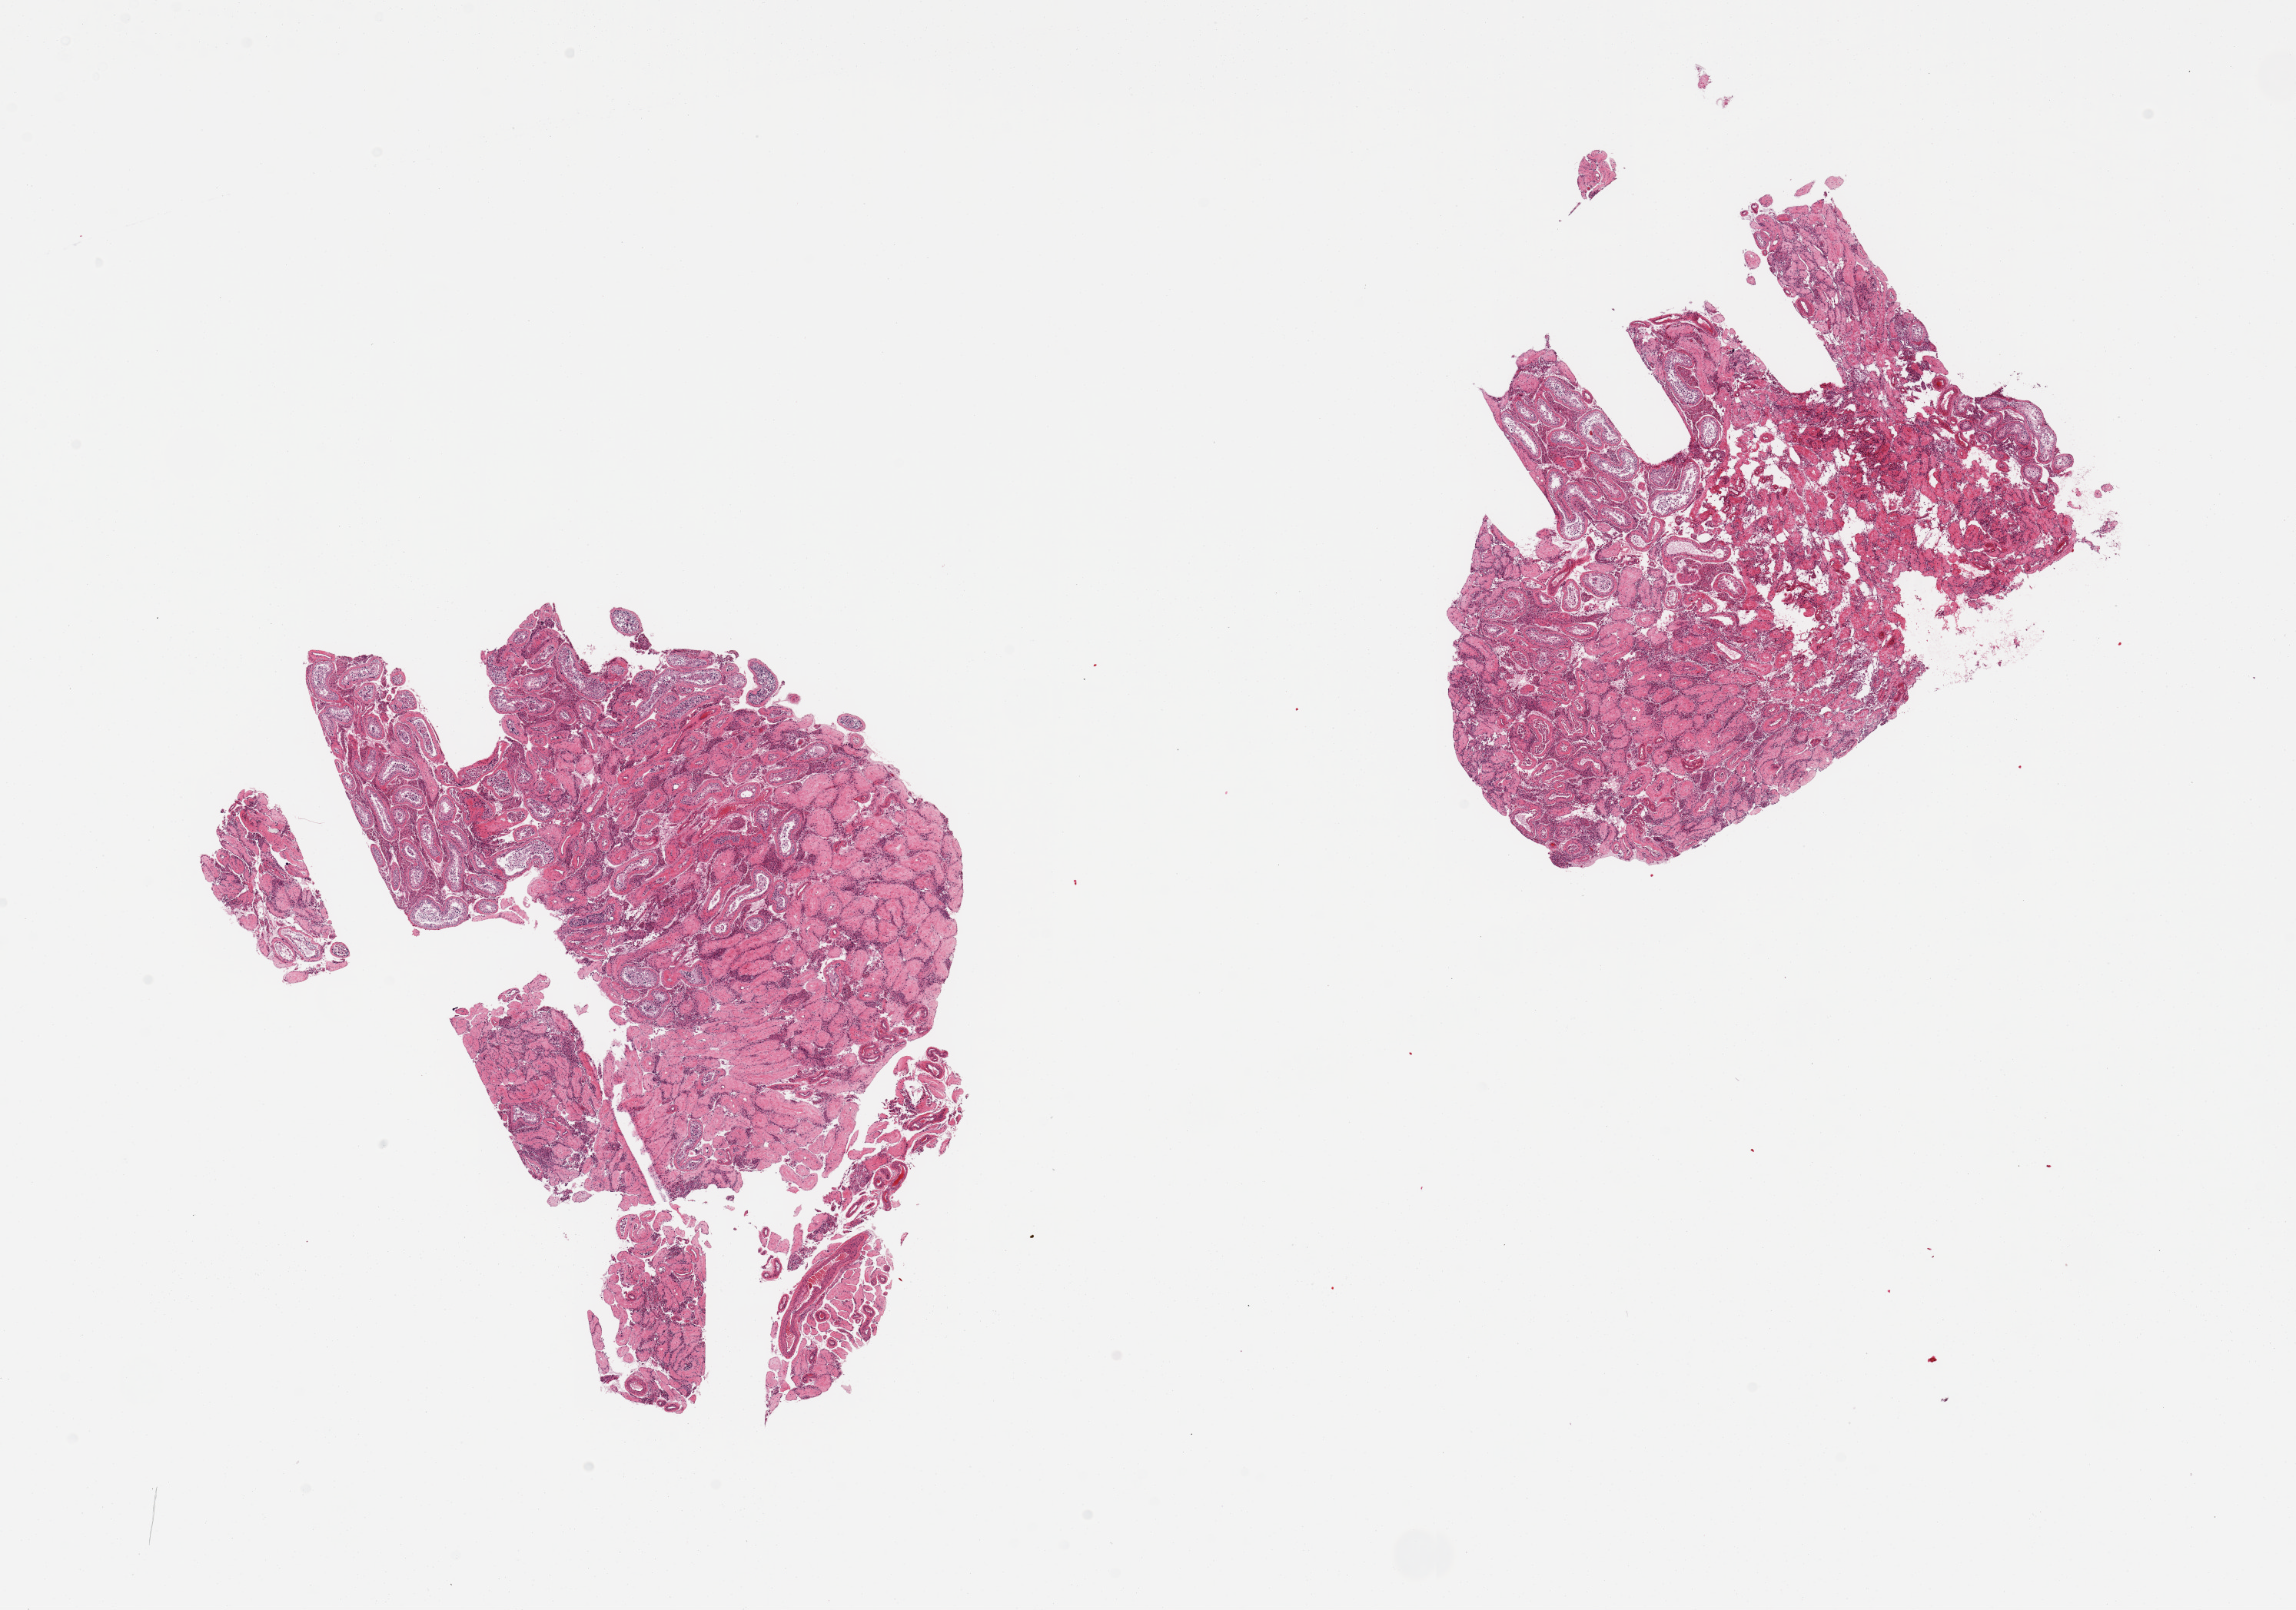
Hematoxylin and eosin (H&E) whole-slide image, brightfield, a low-resolution overview of the entire scanned area, about 23.6 x 16.6 mm (from a 20x scan), PAXgene-fixed, paraffin-embedded tissue, sampled site (target tissue): testis, donor tissue sample. Donor sex: male.
- pathologist's review note for this sample: 2 pieces; mostly hyalinized tubules with Leydig cell hyperplasia; virtually no normal spermatogenesis